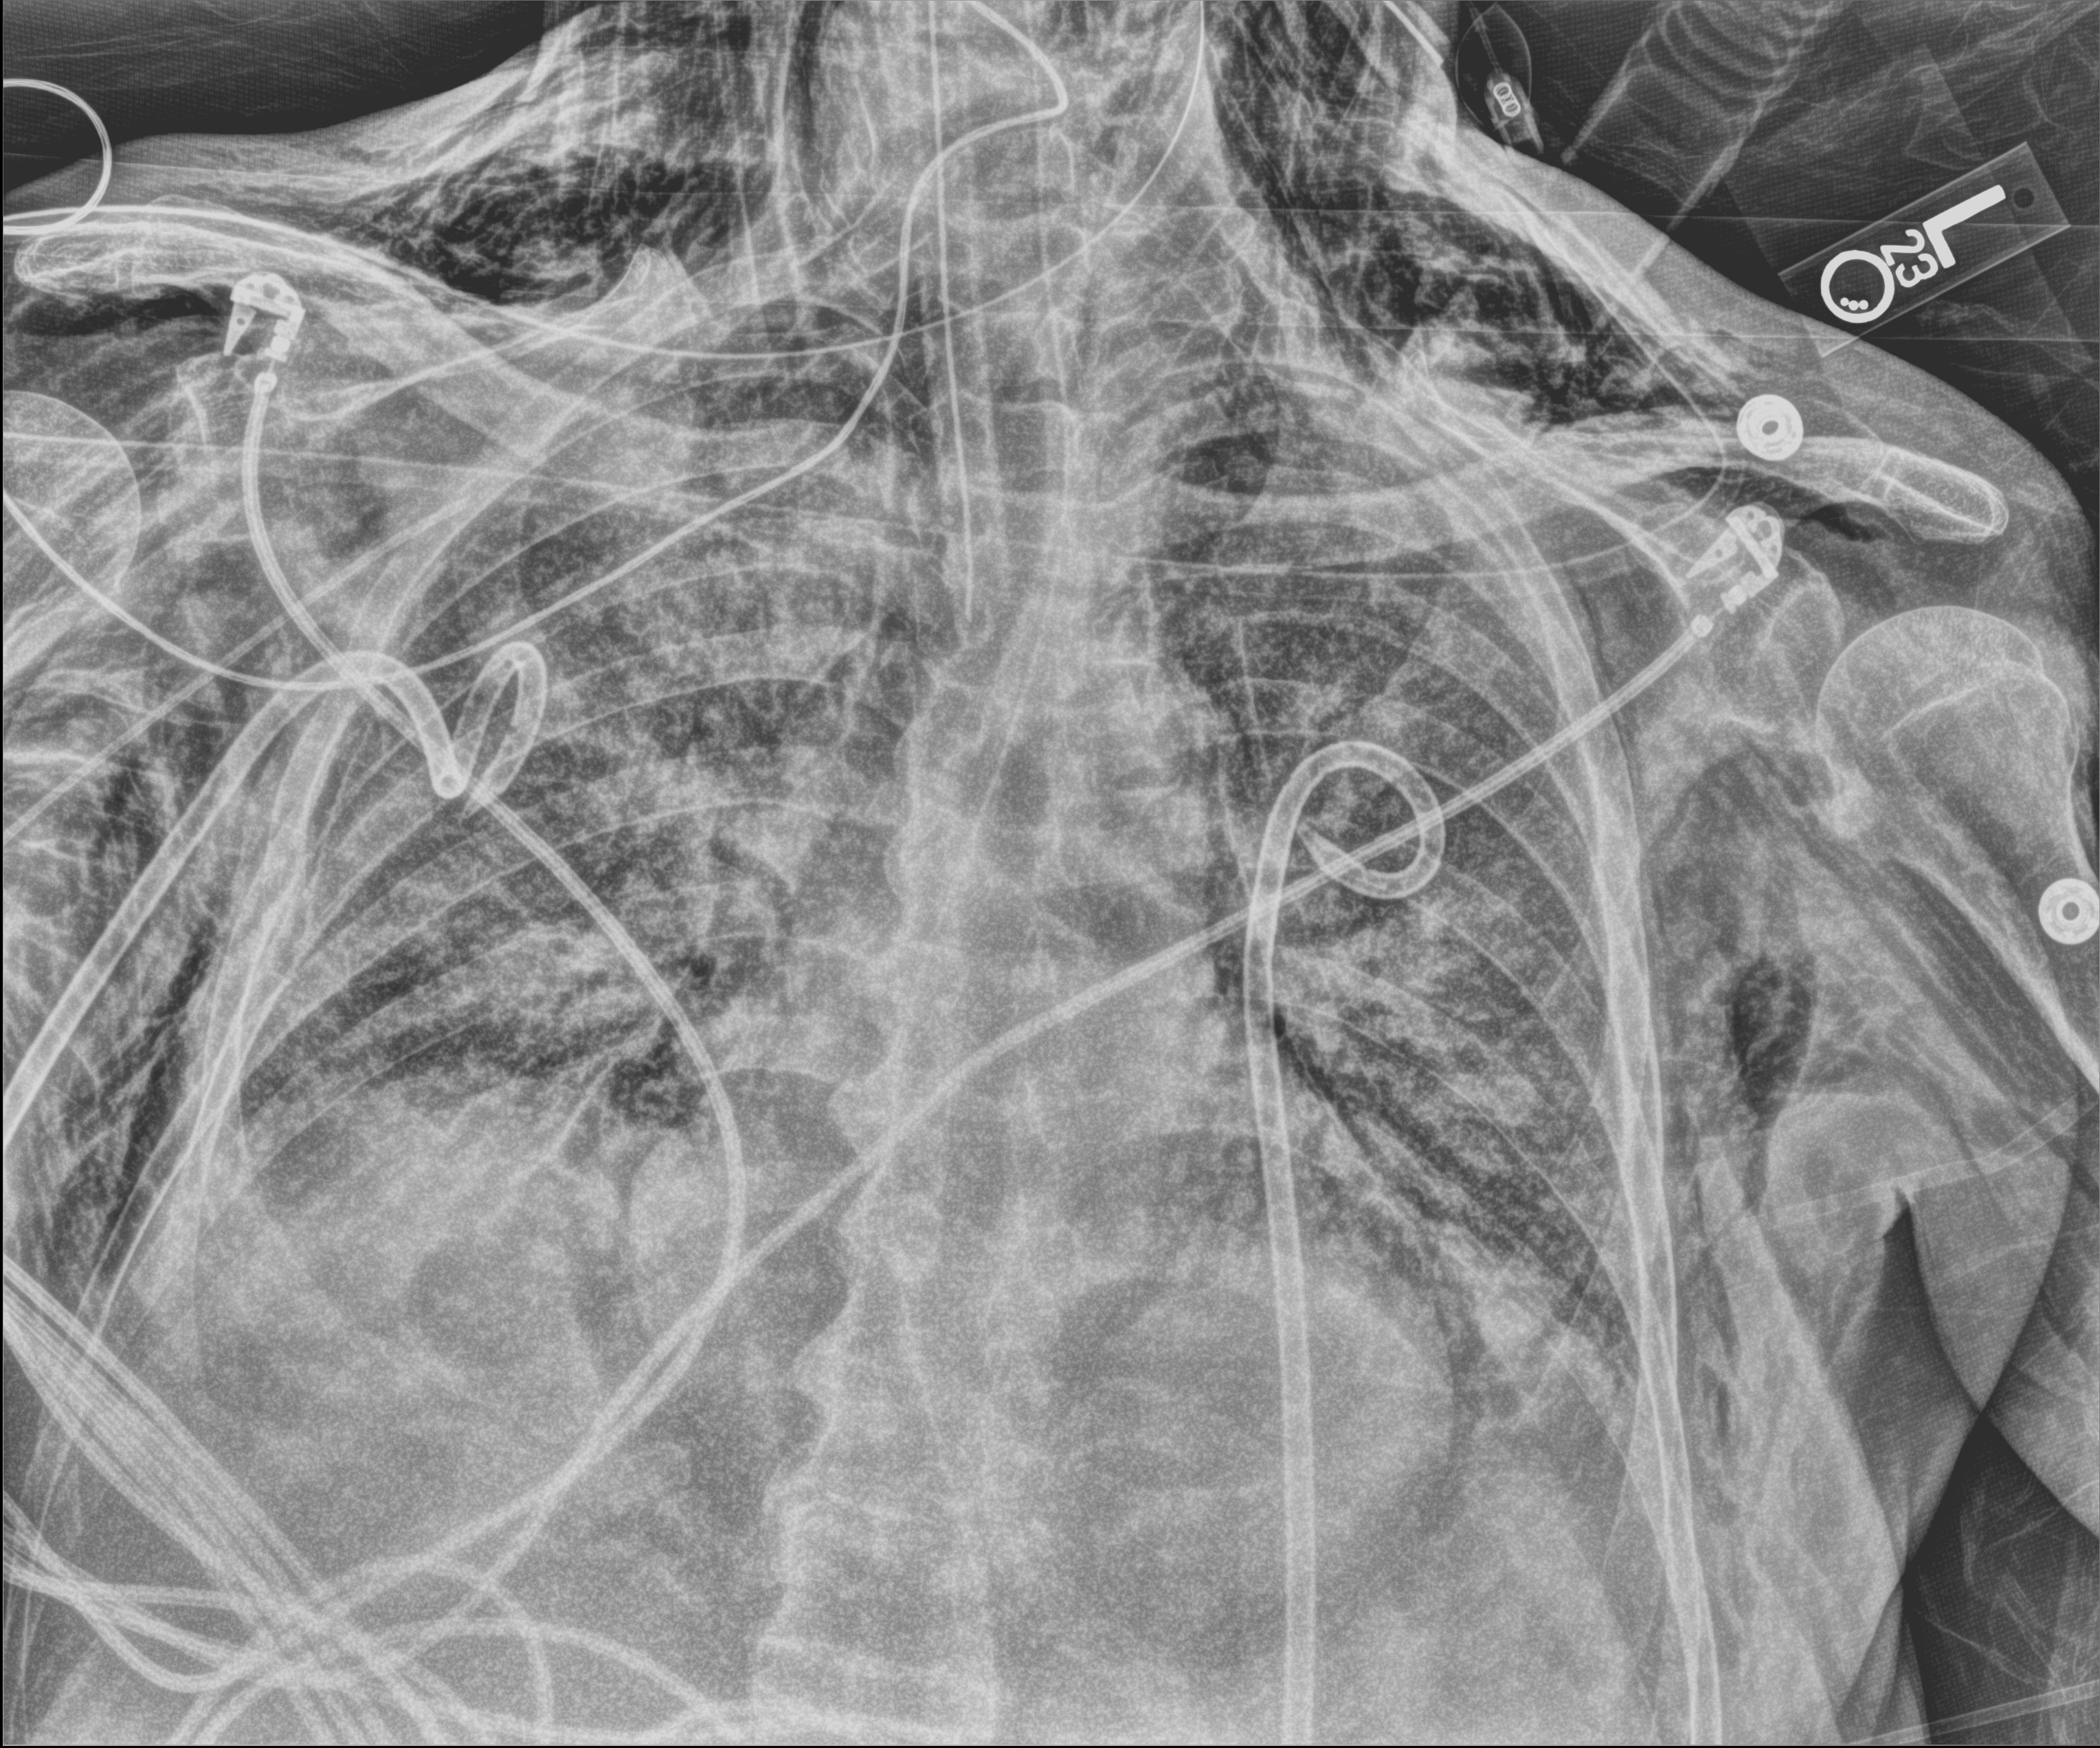
Chest X-ray (portable); anteroposterior (AP) projection. Patient hospitalised with COVID-19; male, aged 75–90 years.
Hospital-stay facts (about this admission, not read from this image; timing relative to this image not recorded): admitted to intensive care during this hospital stay: yes; mechanically ventilated during this hospital stay: yes.